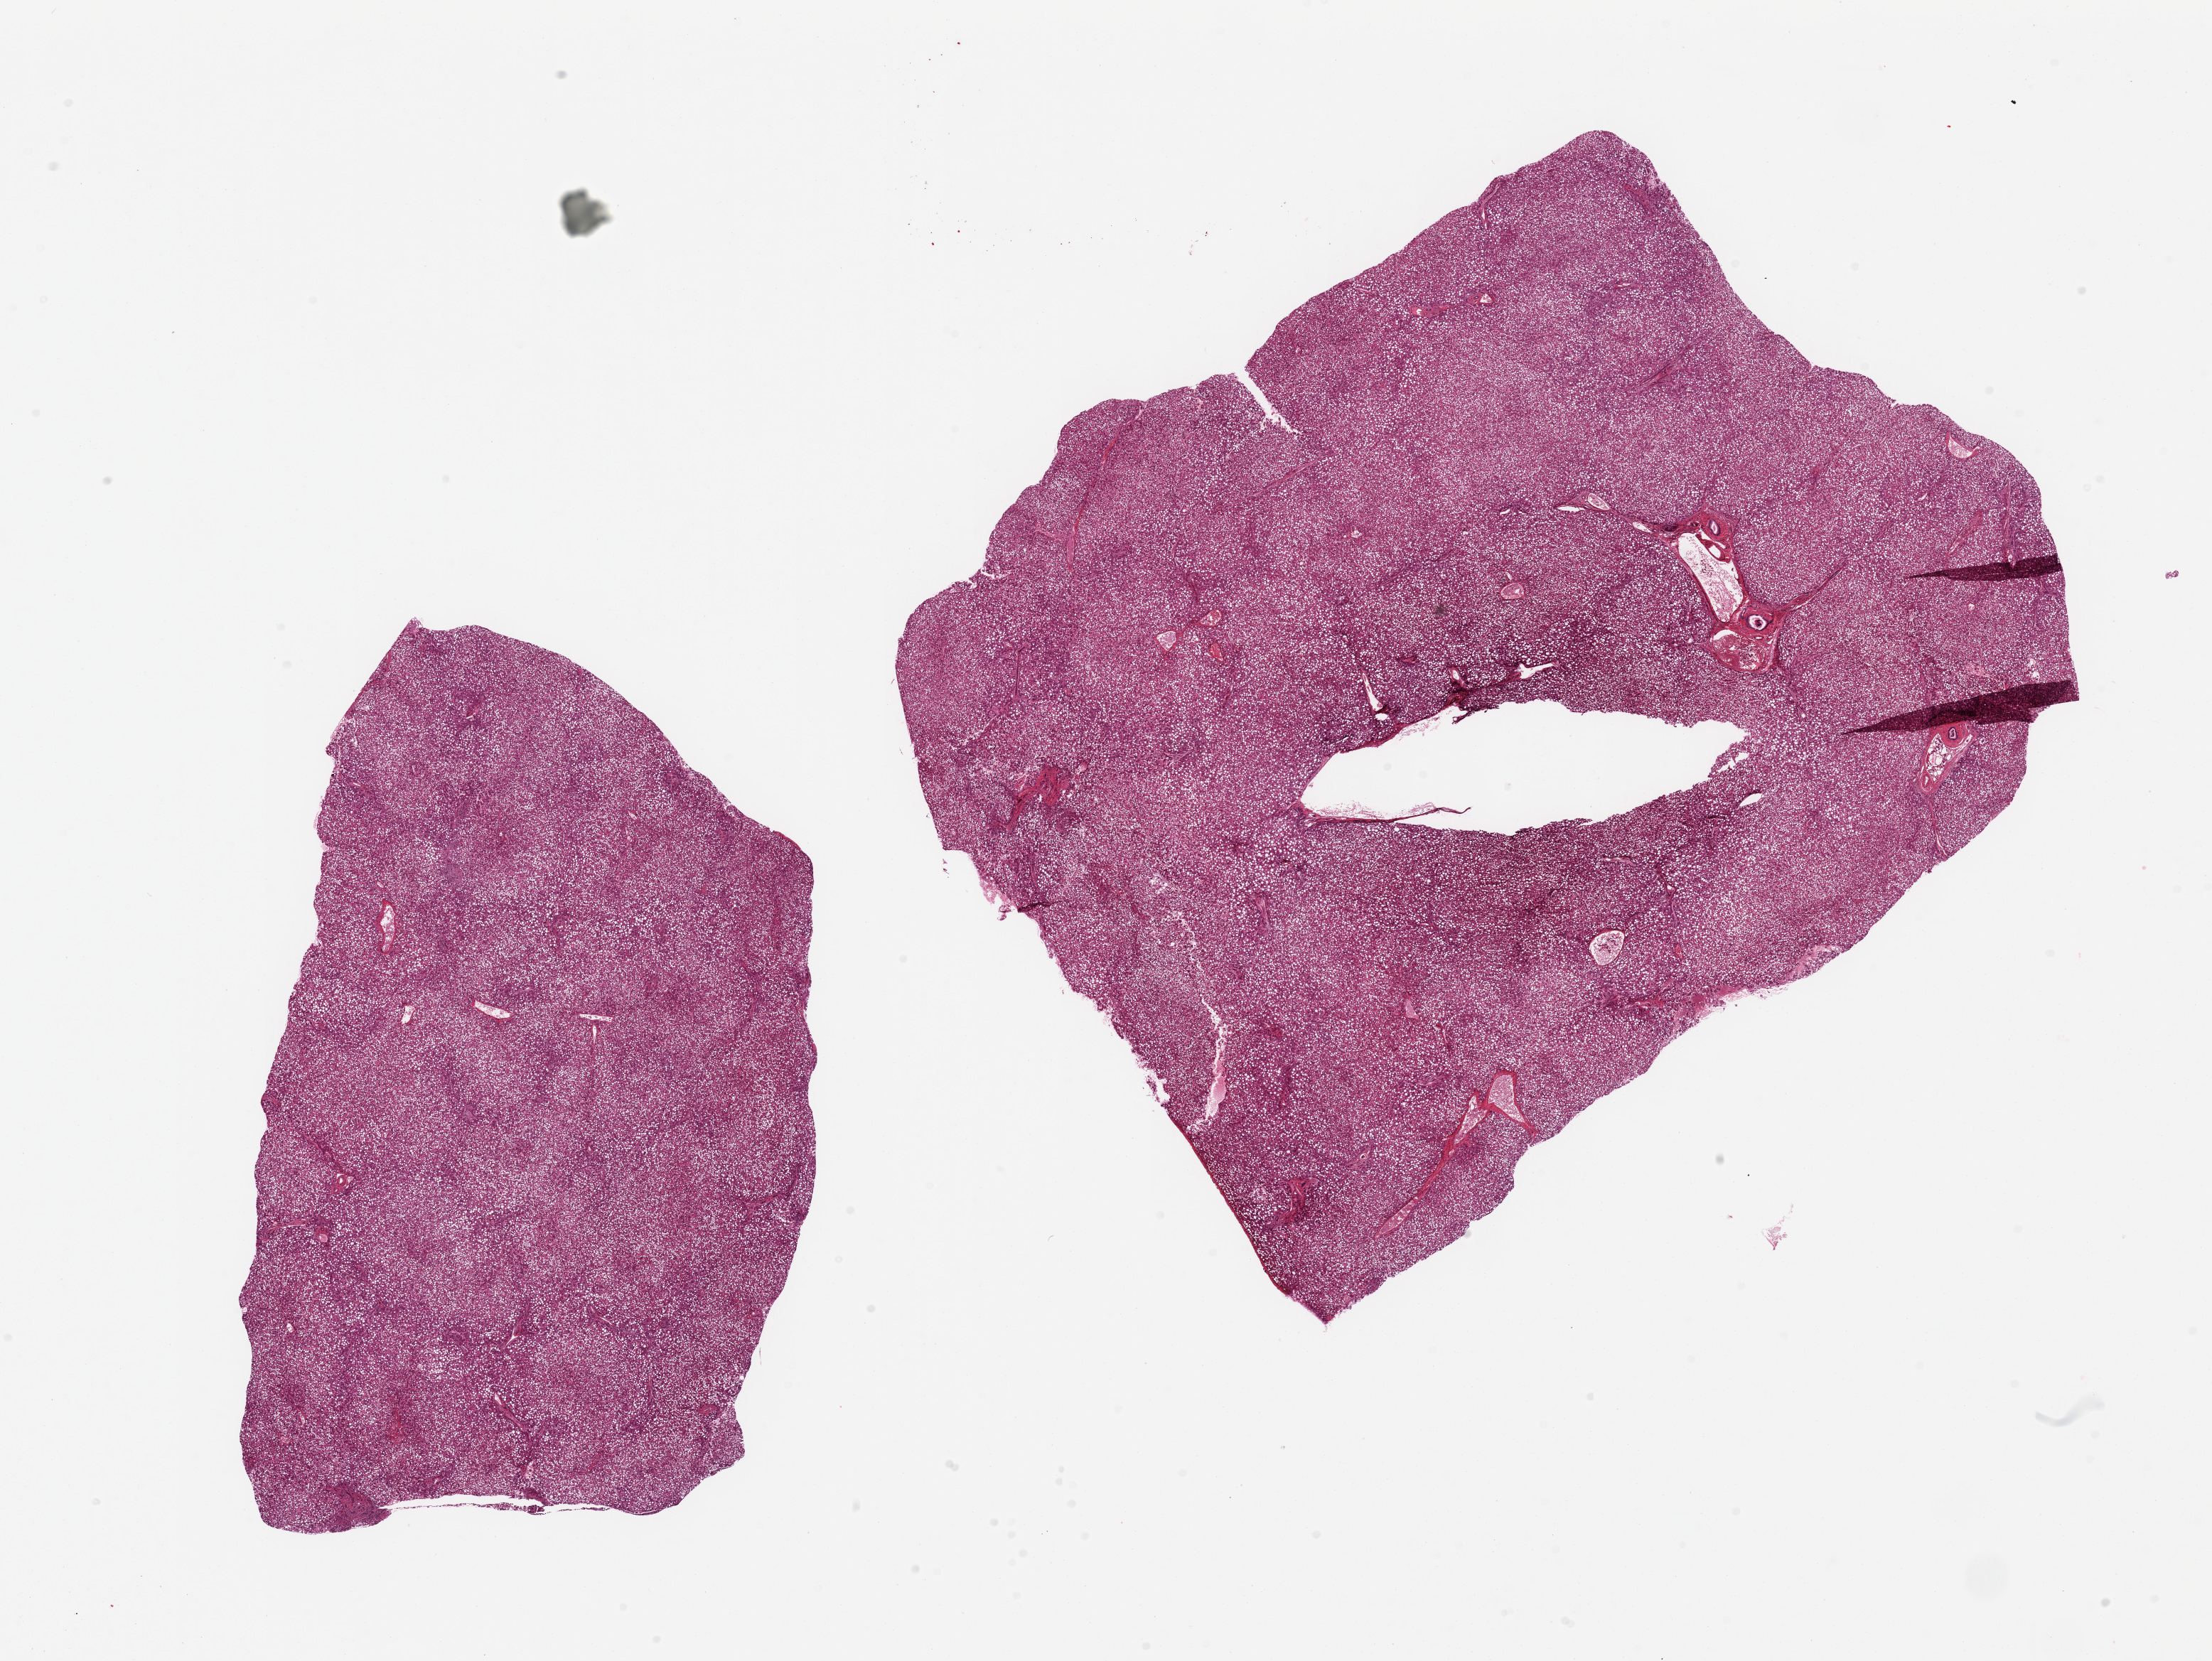
Digitized hematoxylin and eosin (H&E)-stained section, whole scanned area (about 24.6 x 18.5 mm) shown as a low-resolution overview. PAXgene-fixed paraffin-embedded (PFPE) section. Target tissue: liver. Tissue donor sample. Donor sex: female.
• reviewer comment on this tissue sample: 2 pieces, diffuse macrovesicular steatosis, severe, >90% of parenchyma